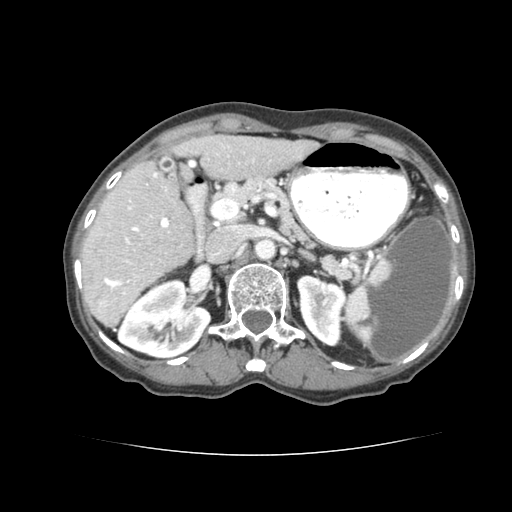
Contrast-enhanced abdominal CT (liver protocol), one axial slice. Slice 39 of 77 in the series (ordered by position). Soft-tissue window (W 400 / L 40 HU). 2.5 mm slice thickness. 512 × 512 image matrix, field of view 340 × 340 mm. Case-level facts recorded for this patient, not image findings: diagnosis: hepatocellular carcinoma (patient treated with transarterial chemoembolisation; whether this scan precedes or follows treatment is not stated here); TNM stage (as recorded): Stage-I; Child-Pugh class: A; tumour nodularity: uninodular; tumour size: 7.6 cm.
Outlined on this slice (semi-automatic segmentation, software-assisted and operator-edited):
- liver parenchyma outside the tumour (the mass and vessels are separate outlines, so this box may not span the whole liver): bounding box (x1, y1, x2, y2) in pixels: (80, 136, 315, 324)
- liver vessels: (101, 155, 210, 280)